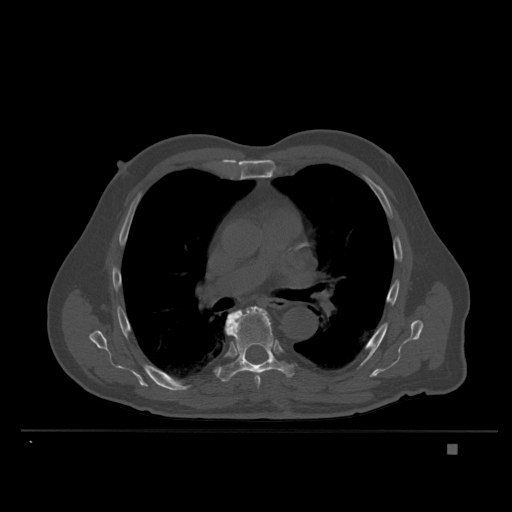
CT including the spine, one axial slice. Slice 247 of 435 in the series (ordered by position). Bone window (W 1800 / L 400 HU). 1.5 mm slice thickness. 512 × 512 image matrix, field of view 434 × 434 mm. Male patient, age 73 years. Case-level facts recorded for this patient, not image findings: primary cancer: skin.
Structures marked on this image (semi-automatic segmentation, software-assisted and operator-edited):
- T6 vertebra: bounding box (x1, y1, x2, y2) in pixels: (226, 310, 261, 387)
- T7 vertebra: (215, 306, 294, 382)